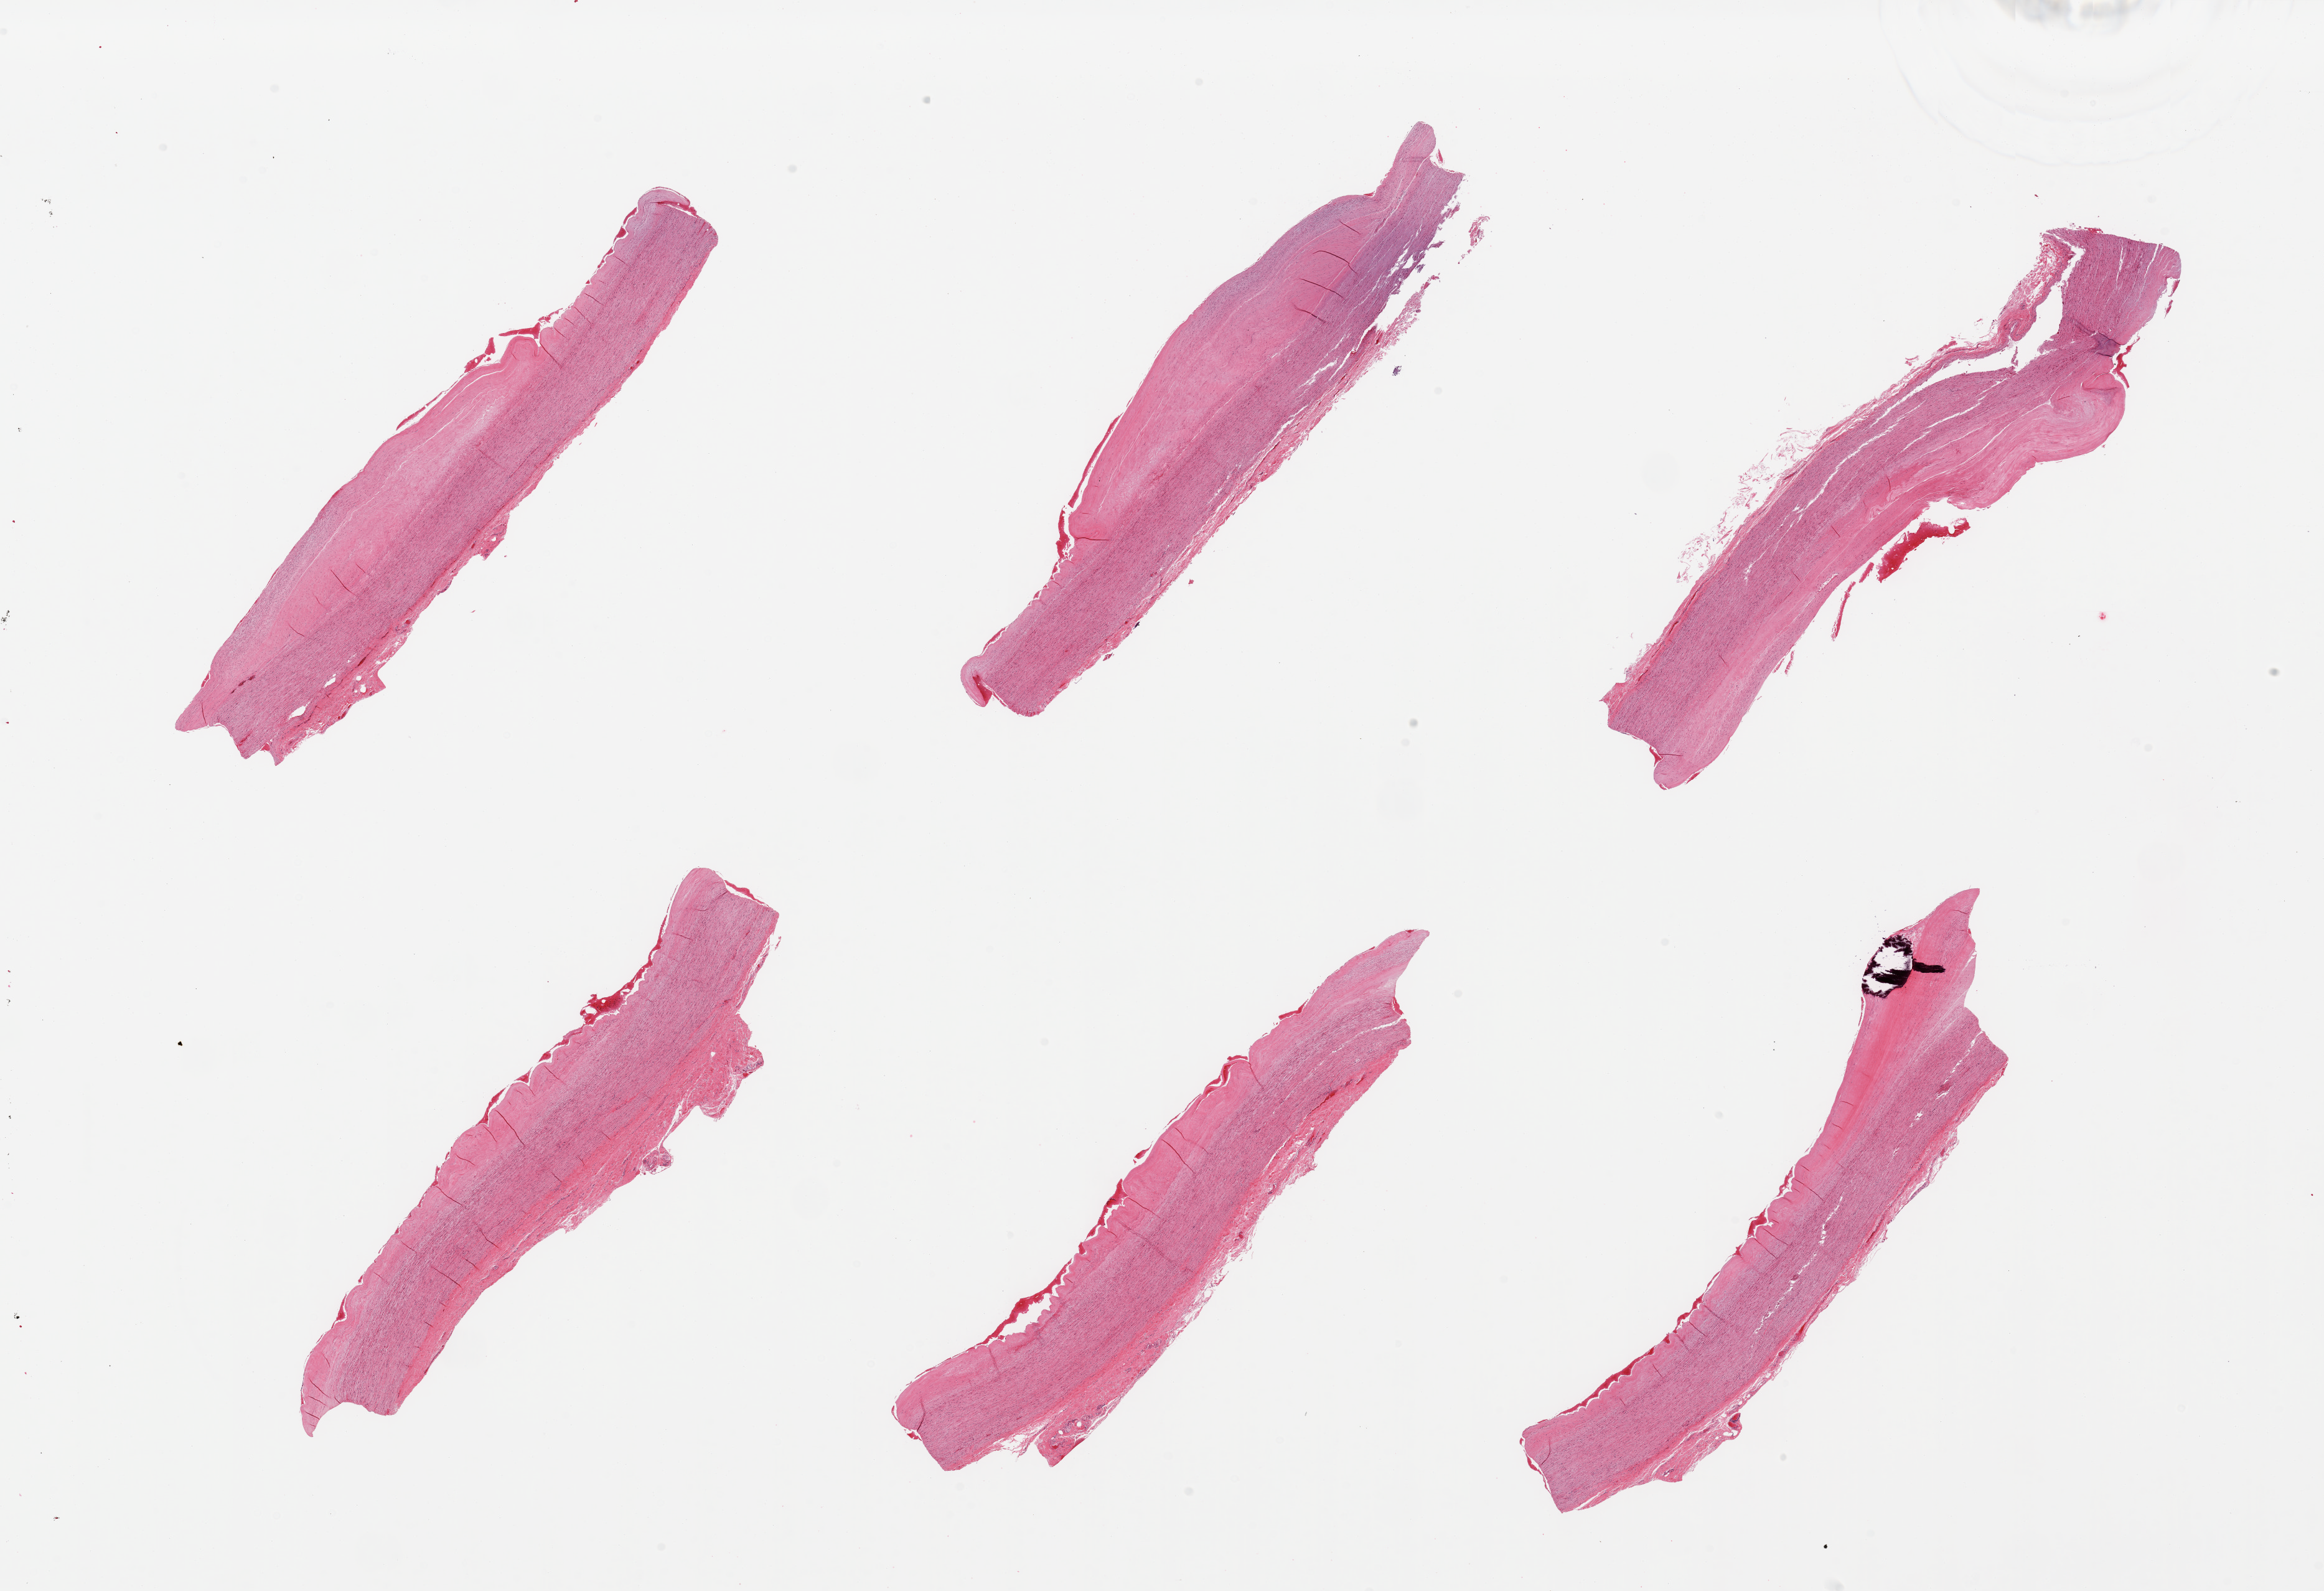
Hematoxylin and eosin (H&E) whole-slide image, brightfield — shown as a low-resolution overview of the whole scanned area (about 29.5 x 20.2 mm). PAXgene-fixed, paraffin-embedded tissue. Sampled site (target tissue): aorta. Donor tissue sample. Donor: female.
• pathologist's review note for this sample: 6 pieces; moderately large, focally calcified fibroatheromatous plaques